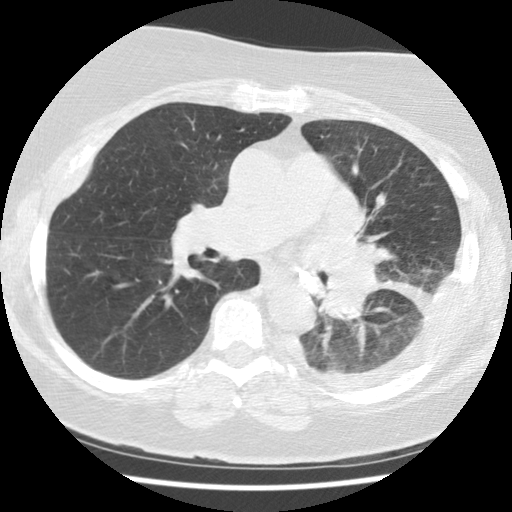
Chest CT (low-dose screening protocol), one axial image. First (baseline) screen. Lung window (W 1500 / L -600 HU). 120 kVp. Female, age 65 years at enrolment.
Expert reader's lesion annotation, bounding box (x1, y1, x2, y2) in pixels: (295, 283, 389, 355). The exam's reader record, not a measurement of the box and not confirmed to be the same lesion: non-calcified nodule or mass ≥4 mm, left lower lobe, 74 × 48 mm, spiculated (stellate) margins, soft tissue attenuation. Later outcome: lung cancer diagnosed 13 days after this screen — adenocarcinoma, NOS, left lower lobe, stage IV (AJCC 6th edition), 74 mm at pathology.